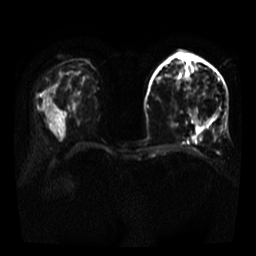
Breast MRI, one axial slice; position 18 of 35 along the scan axis; diffusion-weighted series; image 2 of 4 stored at this slice position (different b-values; order by instance number); 3 T; 5 mm slice thickness; 256 × 256 image matrix, field of view 320 × 320 mm. Female patient.
Outlined on this slice (manually delineated by an expert):
- tumour on diffusion-weighted imaging: box from (x=191, y=109) to (x=203, y=127) px